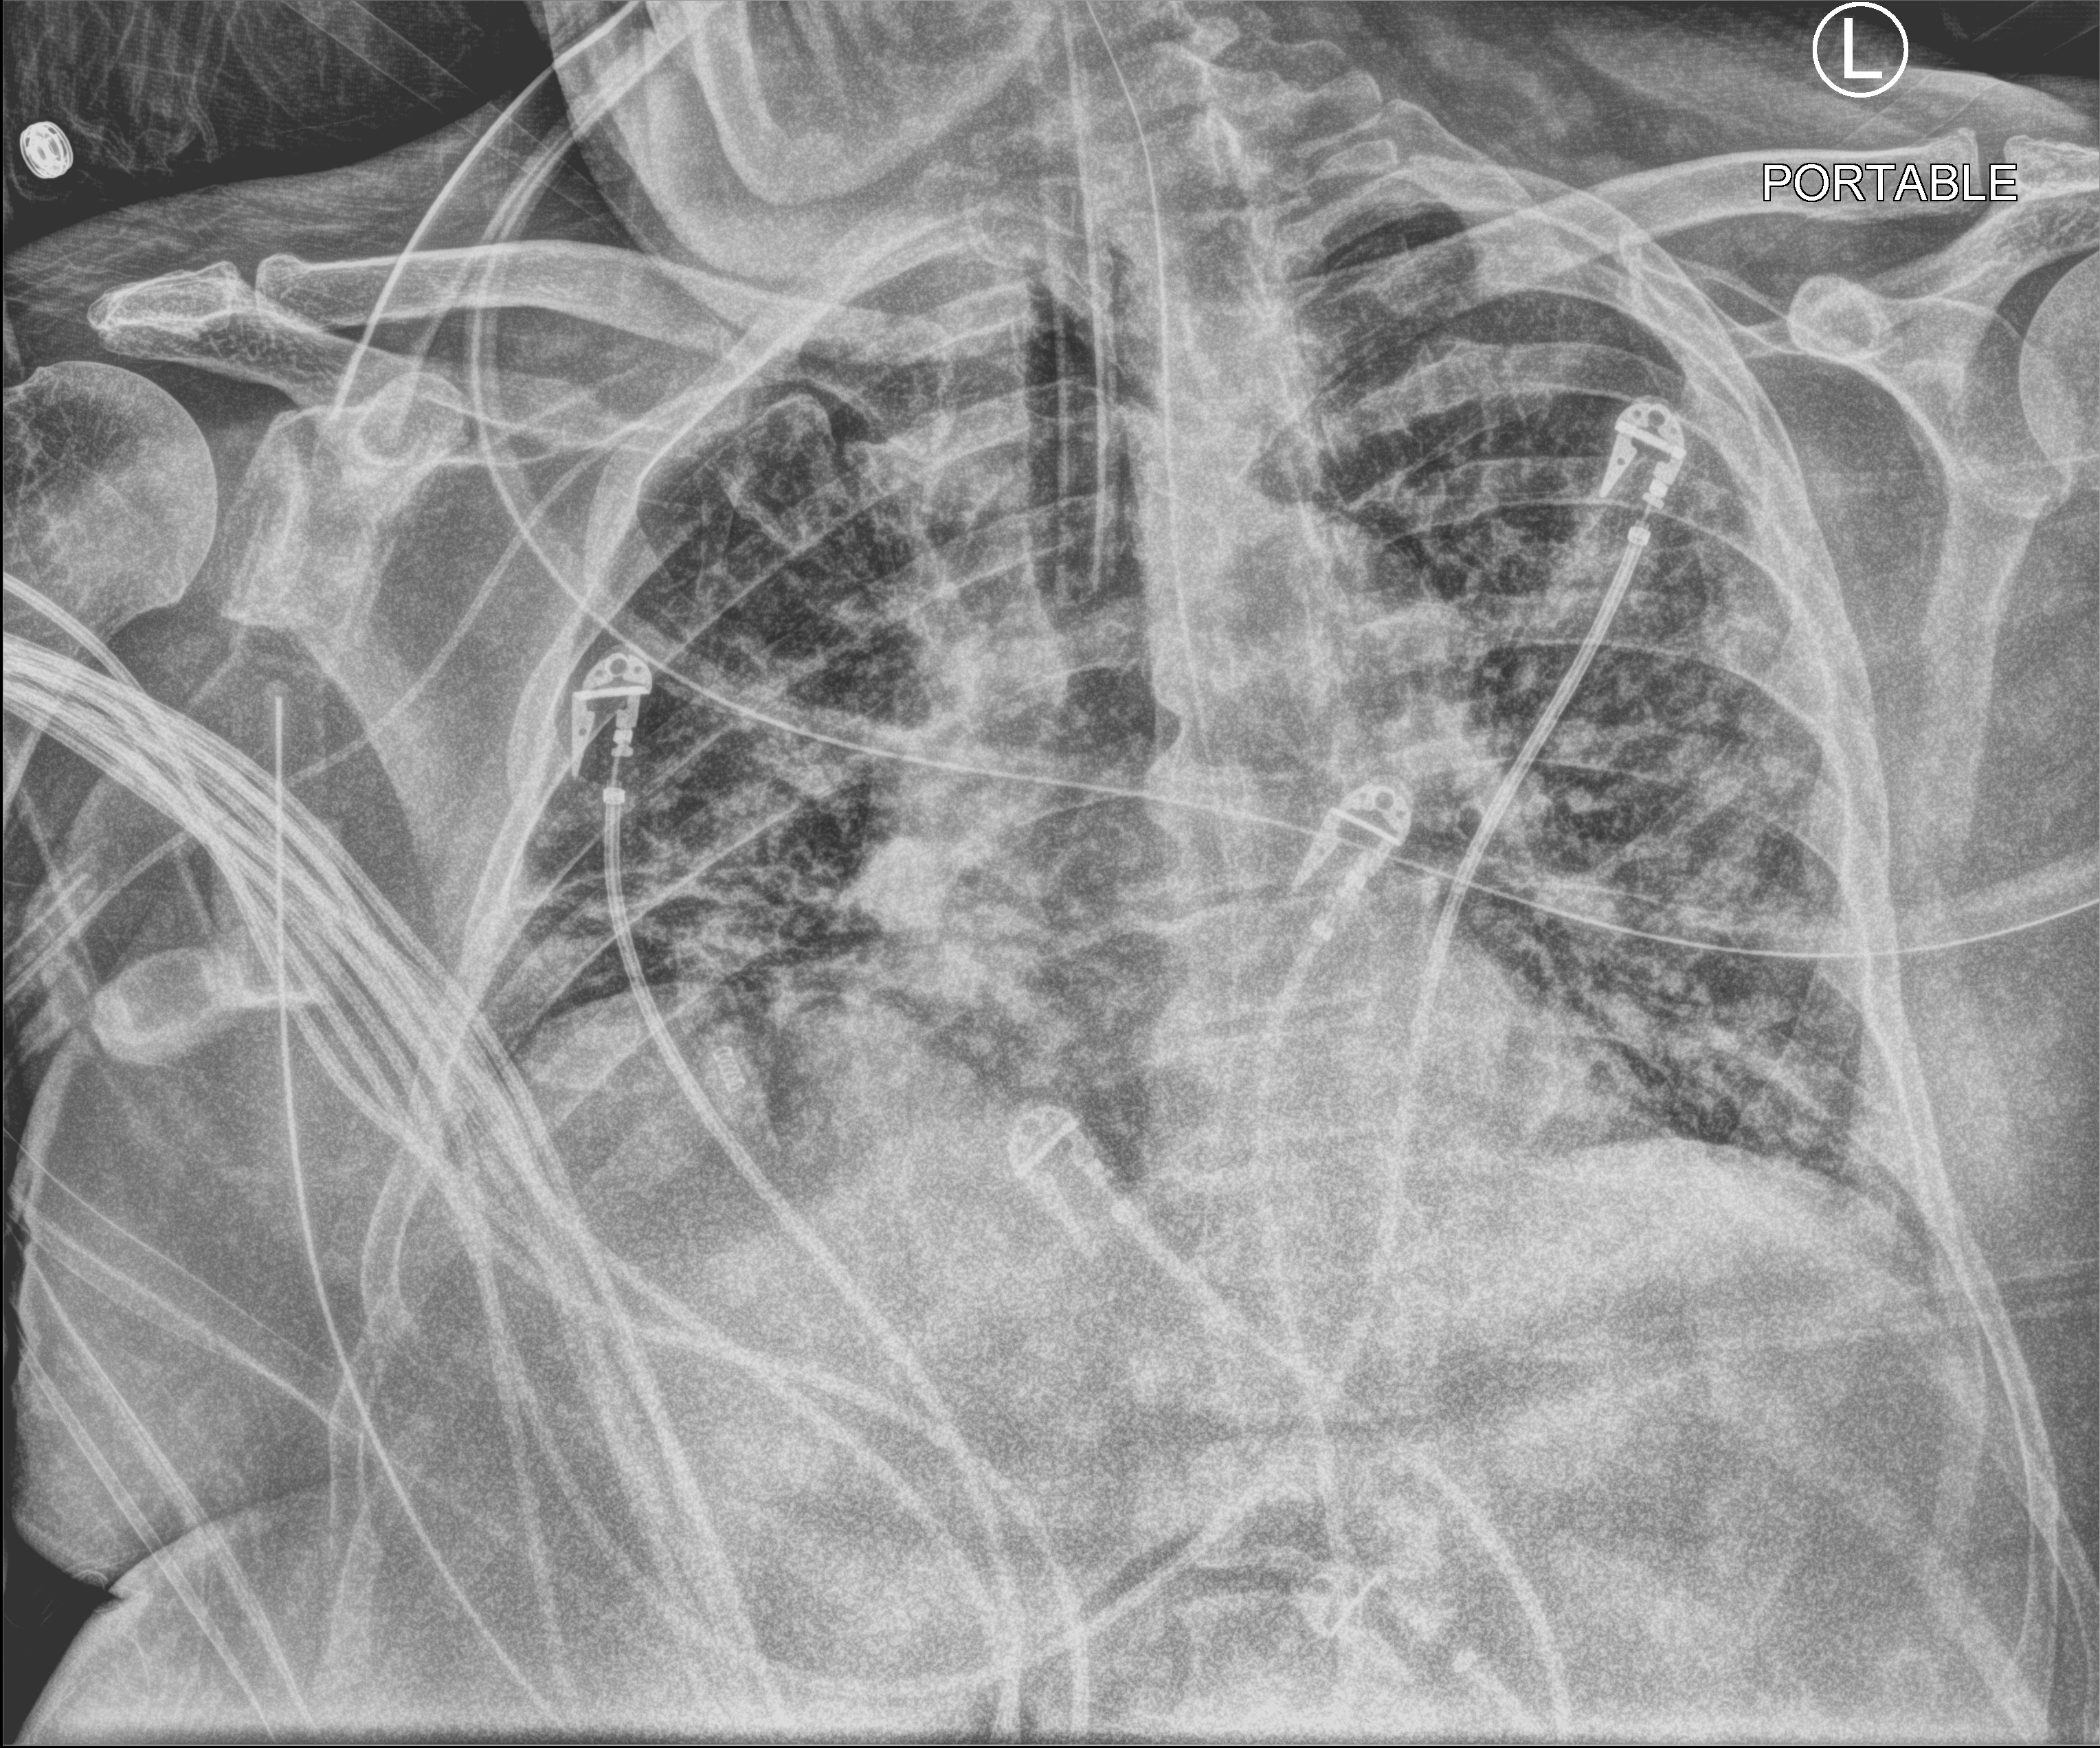
Portable chest radiograph, anteroposterior (AP) projection. Patient hospitalised with COVID-19; male, aged 60–74 years.
Admission-level facts for this patient (not findings on this image; timing relative to this image not recorded):
- admitted to intensive care during this hospital stay: yes